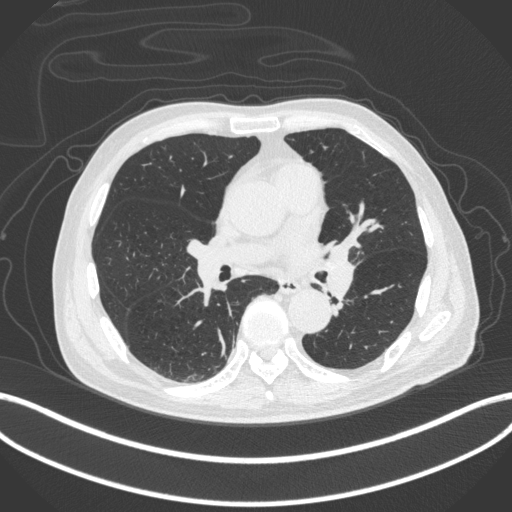
Chest CT, one axial slice; lung window (W 1500 / L -600 HU); 512 × 512 image matrix. Patient: male, 77 years. From the clinical record (not read from this slice): clinical TNM (as recorded): T3 N1 M0.
Outlined on this slice (bounding box drawn by a radiologist):
- lung tumour (recorded histology: adenocarcinoma): bounding box (x1, y1, x2, y2) in pixels: (318, 235, 356, 297)